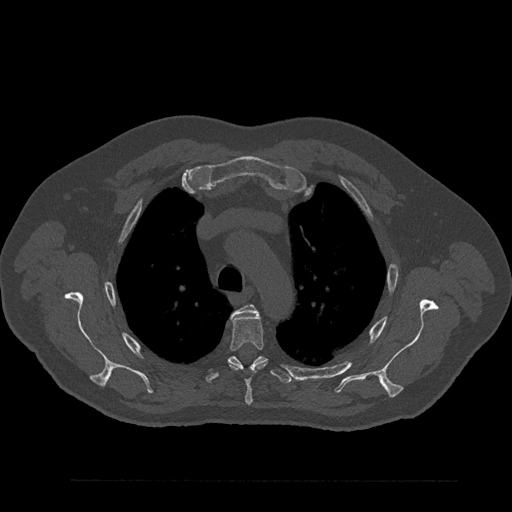
CT including the spine, one axial slice; slice 633 of 797 in the series (ordered by position); reconstruction kernel Br40s/3; bone window (W 1800 / L 400 HU); 512 × 512 image matrix, field of view 430 × 430 mm. Patient: male, 61 years. Case-level facts recorded for this patient, not image findings: primary cancer: prostate.
Outlined on this slice (semi-automatic segmentation, software-assisted and operator-edited):
- T3 vertebra: bounding box (x1, y1, x2, y2) in pixels: (231, 304, 257, 316)
- T4 vertebra: (228, 314, 267, 405)
- T5 vertebra: (205, 356, 292, 384)